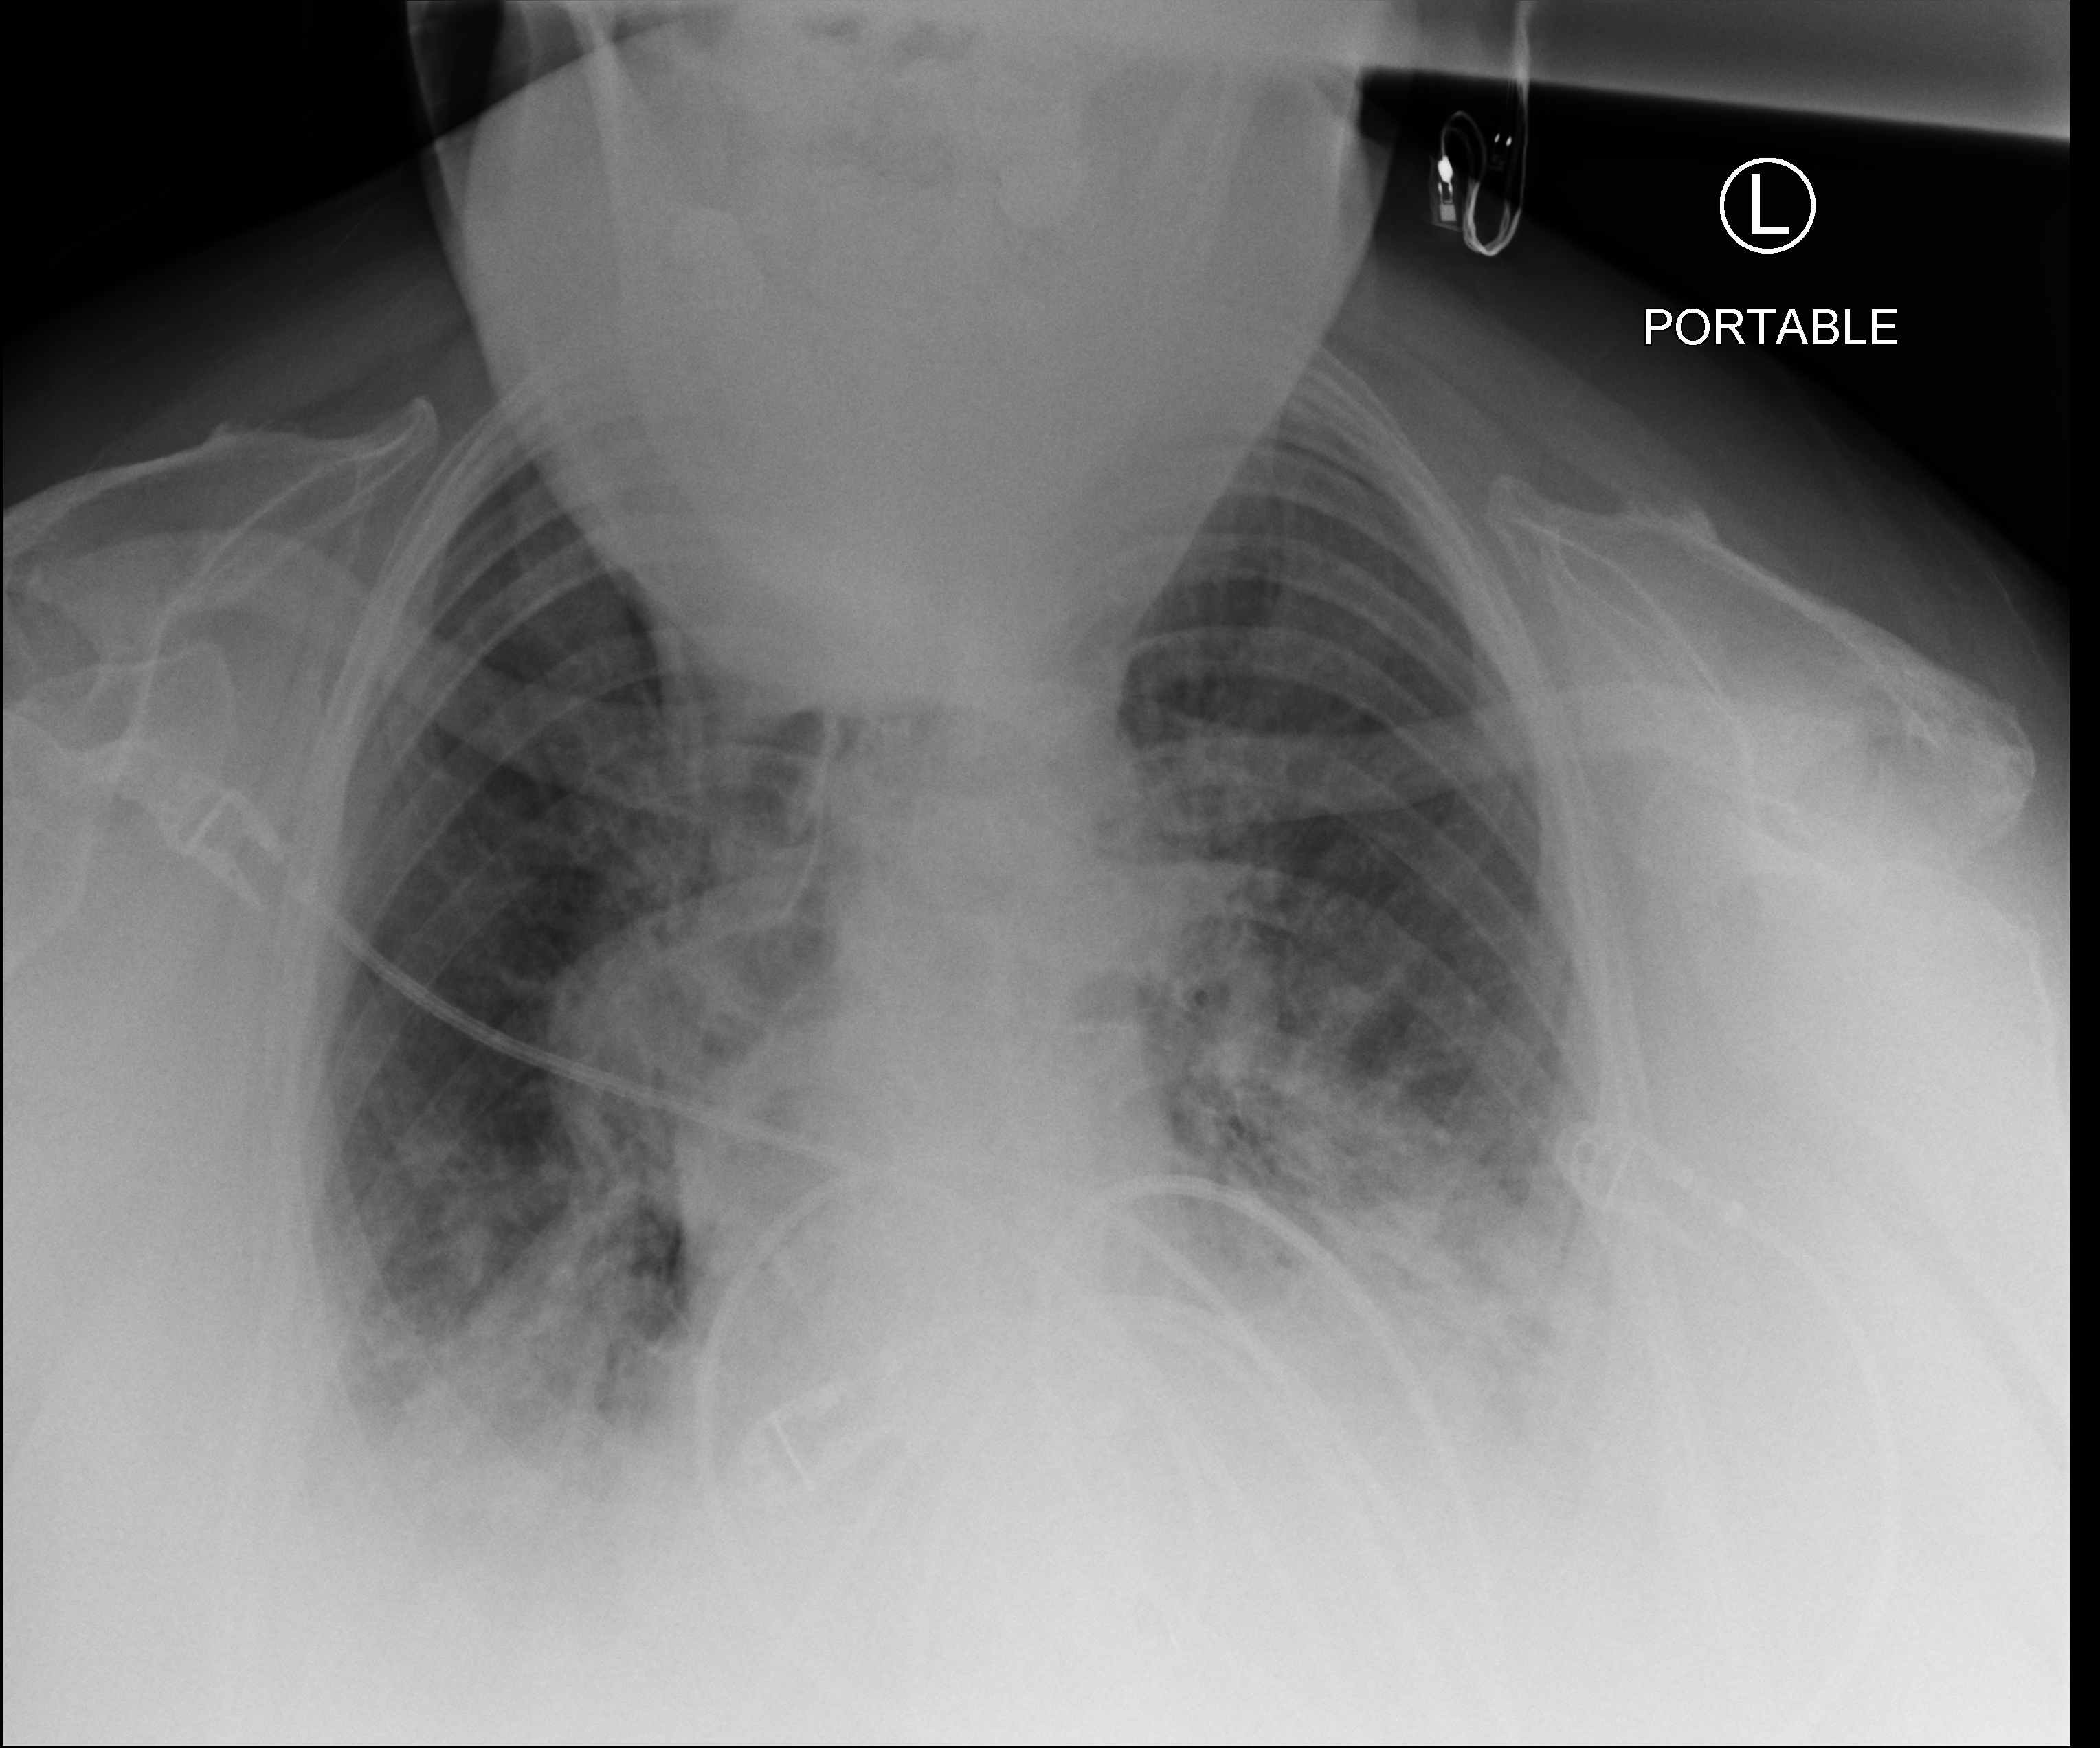
Bedside chest radiograph (computed radiography); anteroposterior (AP) projection. Female patient hospitalised with COVID-19, age 75–90 years.
Admission-level facts for this patient (not findings on this image; timing relative to this image not recorded): admitted to intensive care during this hospital stay: no; mechanically ventilated during this hospital stay: no.